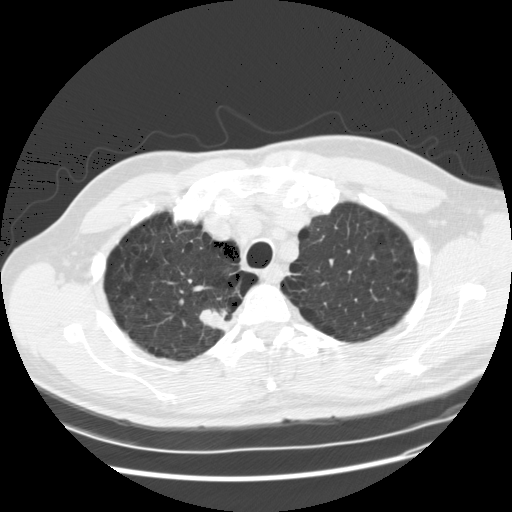
Axial slice from a low-dose chest CT screening exam; baseline annual screen; lung window (W 1500 / L -600 HU); 120 kVp. Male, age 61 years at enrolment. Former smoker at enrolment.
Expert-annotated lung lesion, box from (x=193, y=290) to (x=237, y=340) px. Reader record for this screening exam (exam-level; its link to the box is not recorded): non-calcified nodule or mass ≥4 mm, right upper lobe, 19 × 13 mm, poorly defined margins, soft tissue attenuation.